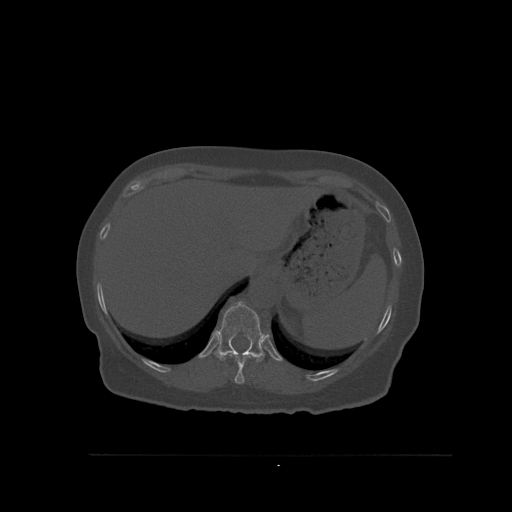
CT including the spine, one axial slice. Position 307 of 527 along the scan axis. Bone window (W 1800 / L 400 HU). 512 × 512 image matrix. Patient: female, 73 years. From the clinical record (not read from this slice): primary cancer: breast.
Outlined on this slice (semi-automatic segmentation, software-assisted and operator-edited):
- T10 vertebra: bounding box <229,354,255,384> (left, top, right, bottom; pixels)
- T11 vertebra: <214,301,265,362>